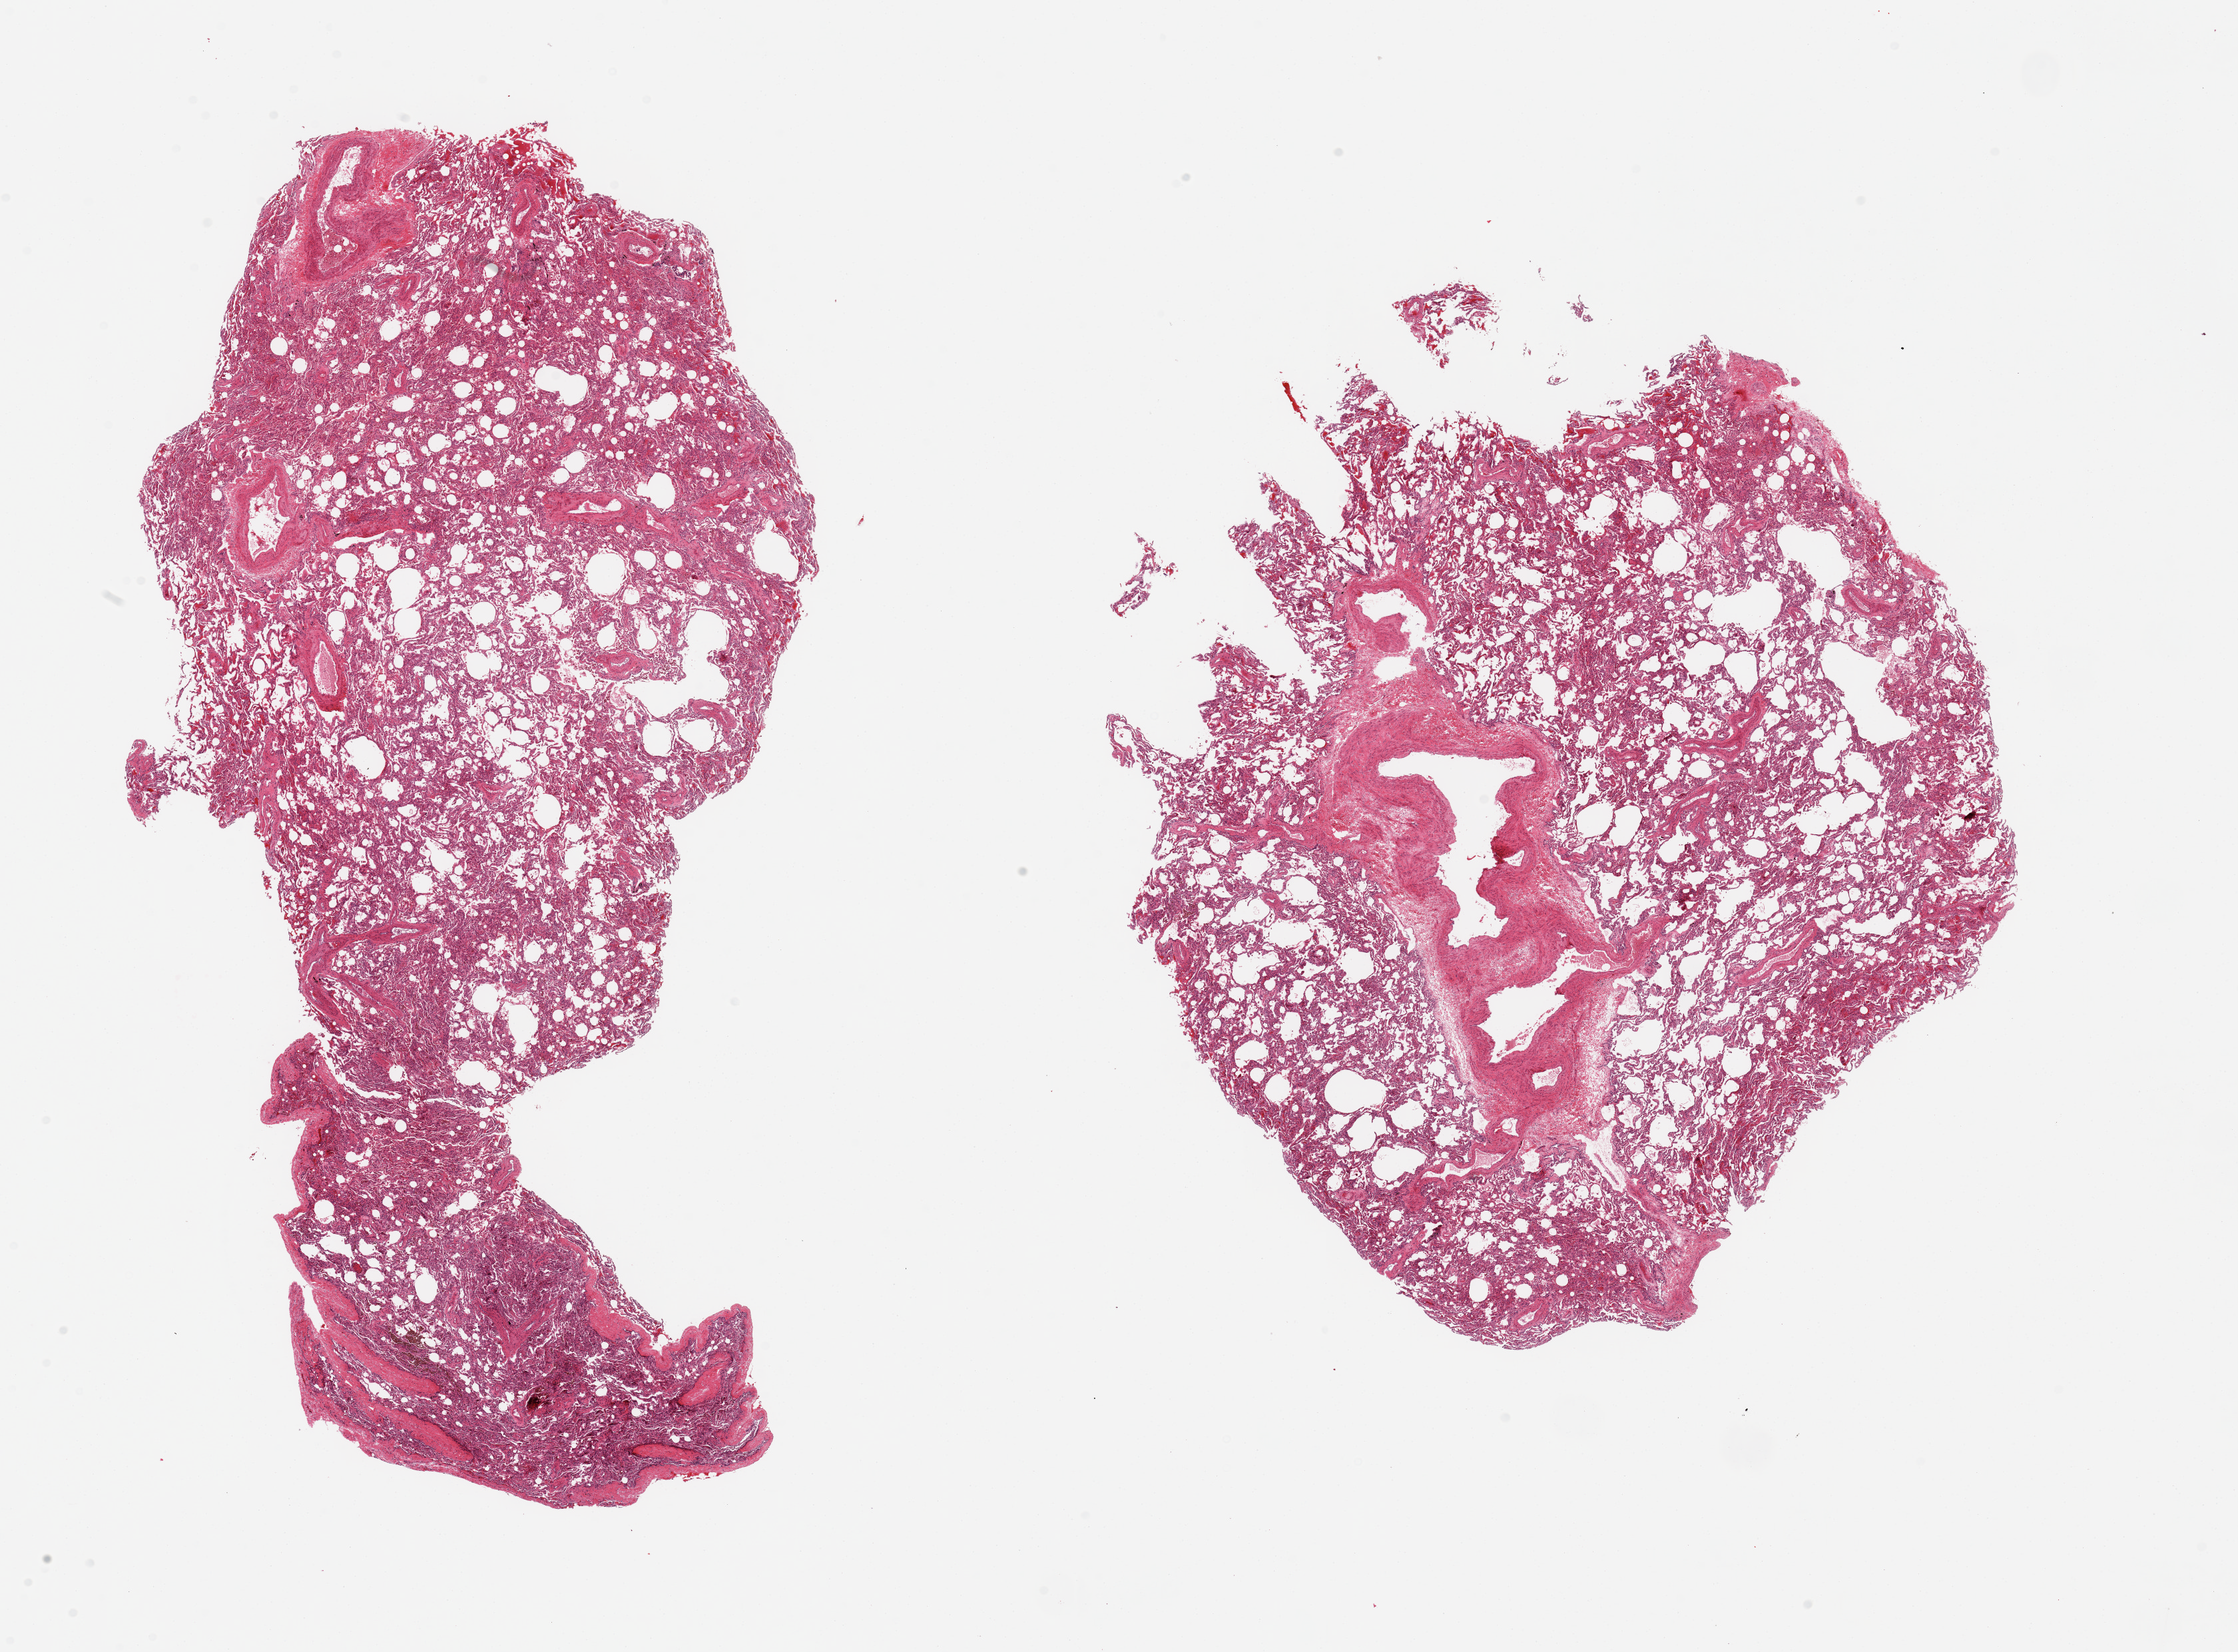
Hematoxylin and eosin (H&E) whole-slide image, brightfield, low-resolution overview of the scanned area, about 26.6 x 19.6 mm (acquisition: 20x scan); PAXgene-fixed, paraffin-embedded tissue; target tissue: lung; tissue donor sample. Donor sex: male.
Review note (as recorded): 2 pieces, moderate congestion.